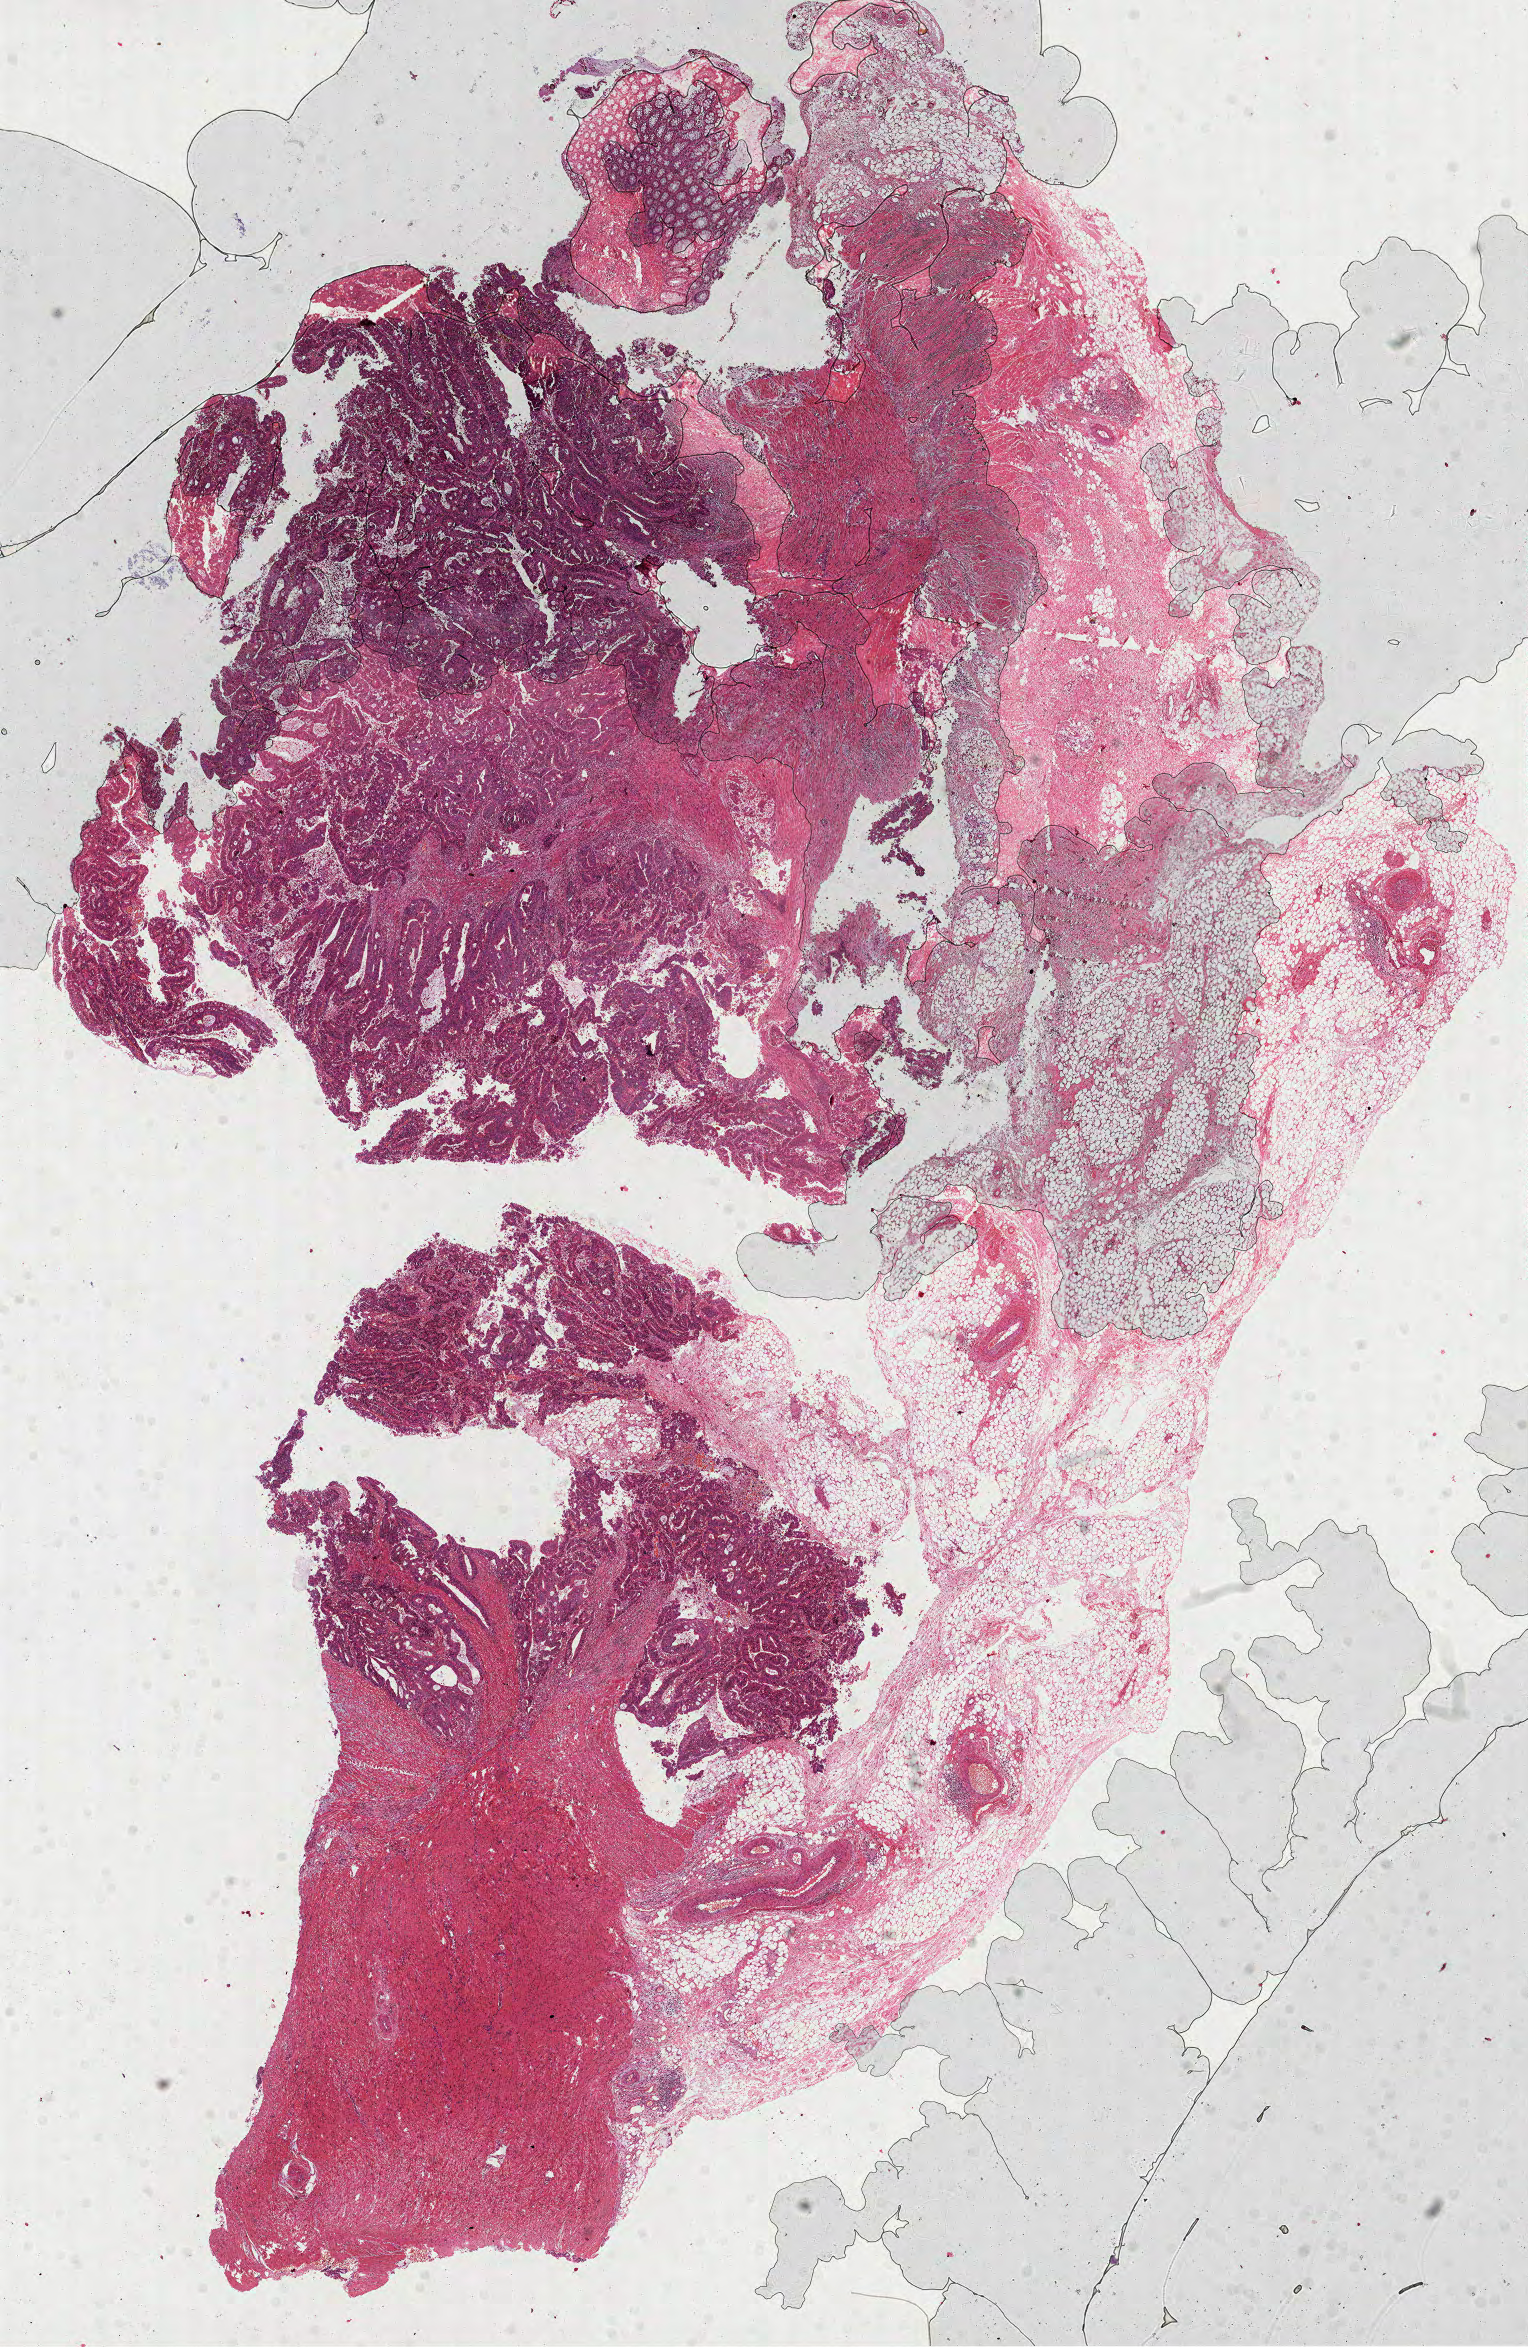
Whole-slide histology image, Hematoxylin and eosin (H&E) stained — whole scanned area (about 12.3 x 18.9 mm, slide scanned at 40x) shown as a low-resolution overview, FFPE section, colon, primary tumour sample. Male, age 56 years at initial diagnosis.
Pathologic diagnosis: Adenocarcinoma, NOS. AJCC pathologic stage: IIA.